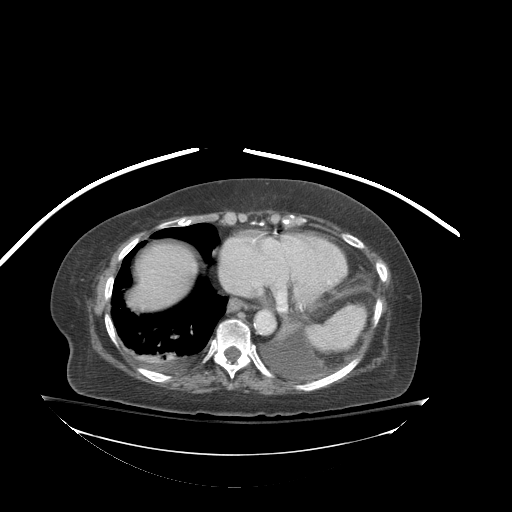
Contrast-enhanced abdominal CT (liver protocol), one axial slice; position 81 of 81 along the scan axis; soft-tissue window (W 400 / L 40 HU); 2.5 mm slice thickness; 512 × 512 image matrix, field of view 500 × 500 mm. From the clinical record (not read from this slice): diagnosis: hepatocellular carcinoma (patient treated with transarterial chemoembolisation; whether this scan precedes or follows treatment is not stated here); TNM stage (as recorded): Stage-I; Child-Pugh class: B; tumour differentiation: well-moderately differentiated; tumour nodularity: uninodular.
Structures marked on this image (semi-automatic segmentation, software-assisted and operator-edited):
- liver parenchyma outside the tumour (the mass and vessels are separate outlines, so this box may not span the whole liver): box from (x=130, y=242) to (x=196, y=310) px